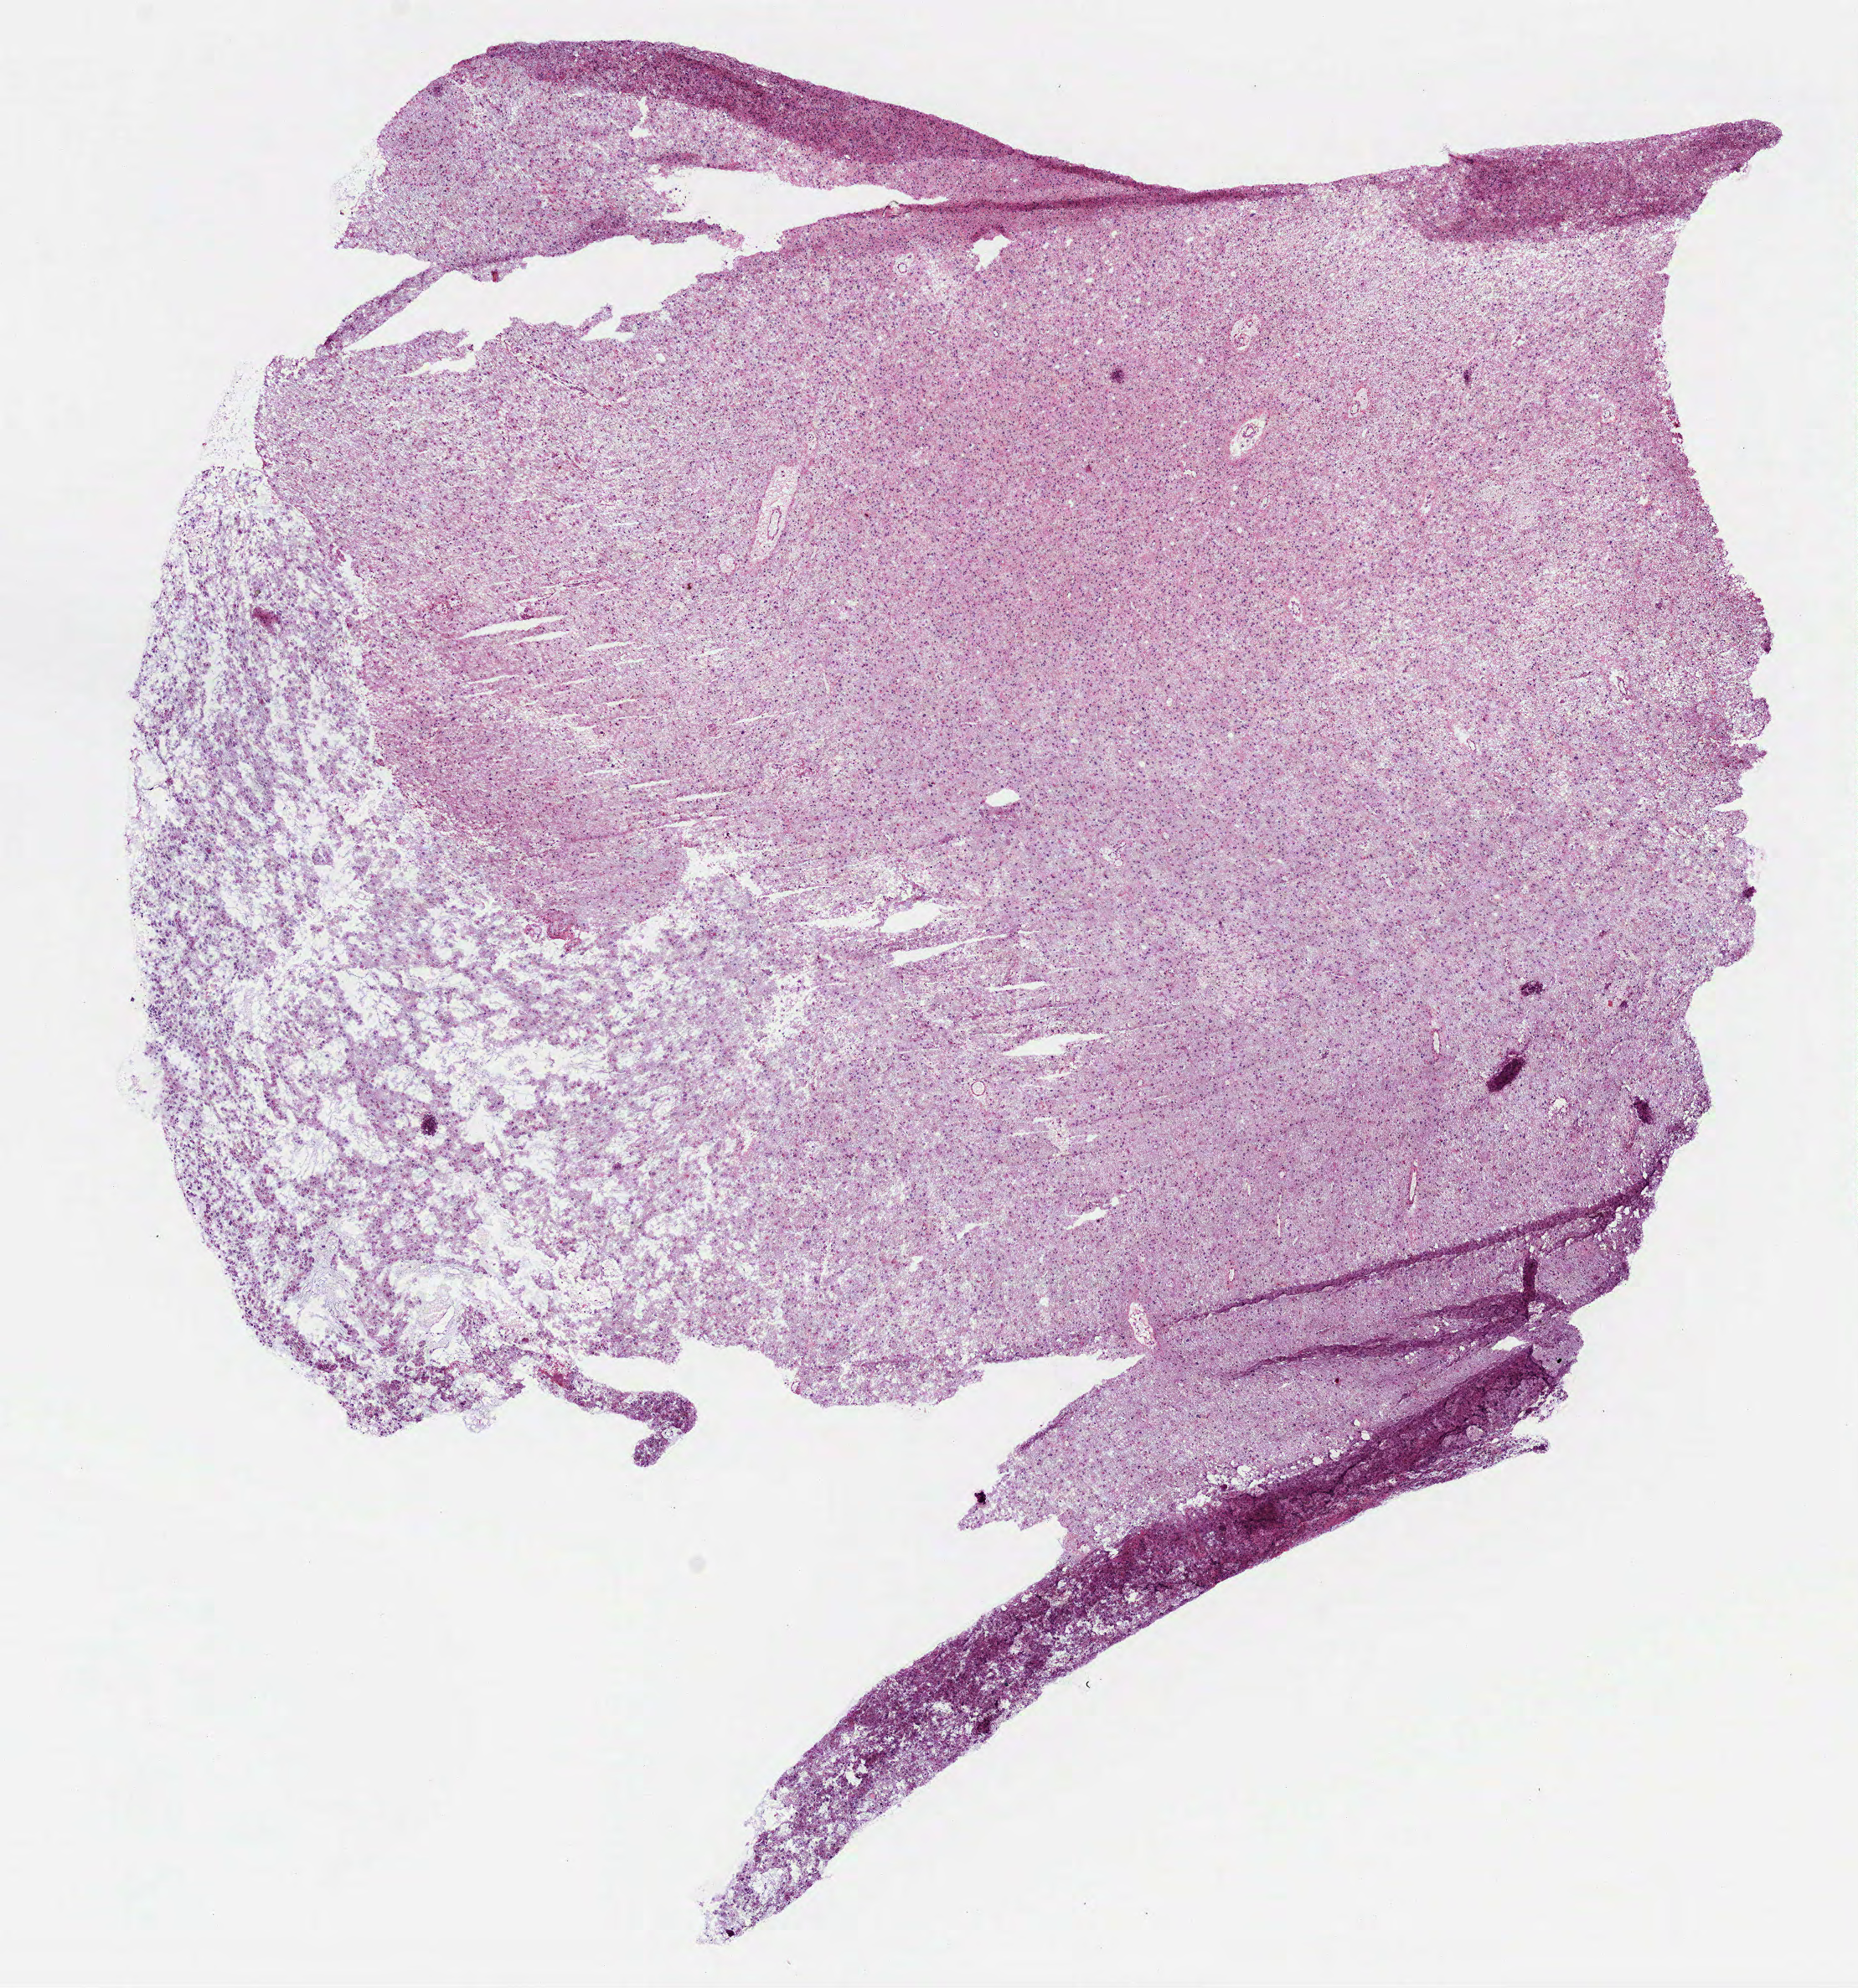
Digitized Hematoxylin and eosin (H&E) stained tissue section (whole slide), low-resolution overview of the scanned area, about 8.9 x 9.6 mm (acquisition: 40x scan); frozen section from the top of the tissue portion; sample: primary tumour, brain. Patient: male, age at initial diagnosis 43 years. Histologic grade: G3 (poorly differentiated). Slide review estimates, as recorded: tumour cells 100%, tumour nuclei 75%, normal cells 0%, stromal cells 0%, necrosis 0%.
Laterality: left. Histologic diagnosis: Mixed glioma (cerebrum).